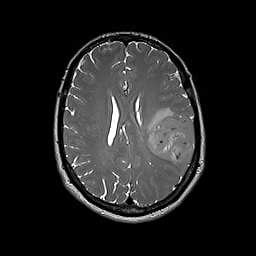
Brain MRI from a brain-tumour surgery series, one axial slice; position 83 of 192 along the scan axis; 256 × 256 image matrix, field of view 250 × 250 mm. Case-level facts recorded for this patient, not image findings: histopathology: Glioblastoma; WHO grade: 4; IDH mutation: no; tumour location: Left Frontal.
Structures marked on this image (expert manual segmentation):
- tumour: bounding box <147,115,195,165> (left, top, right, bottom; pixels)